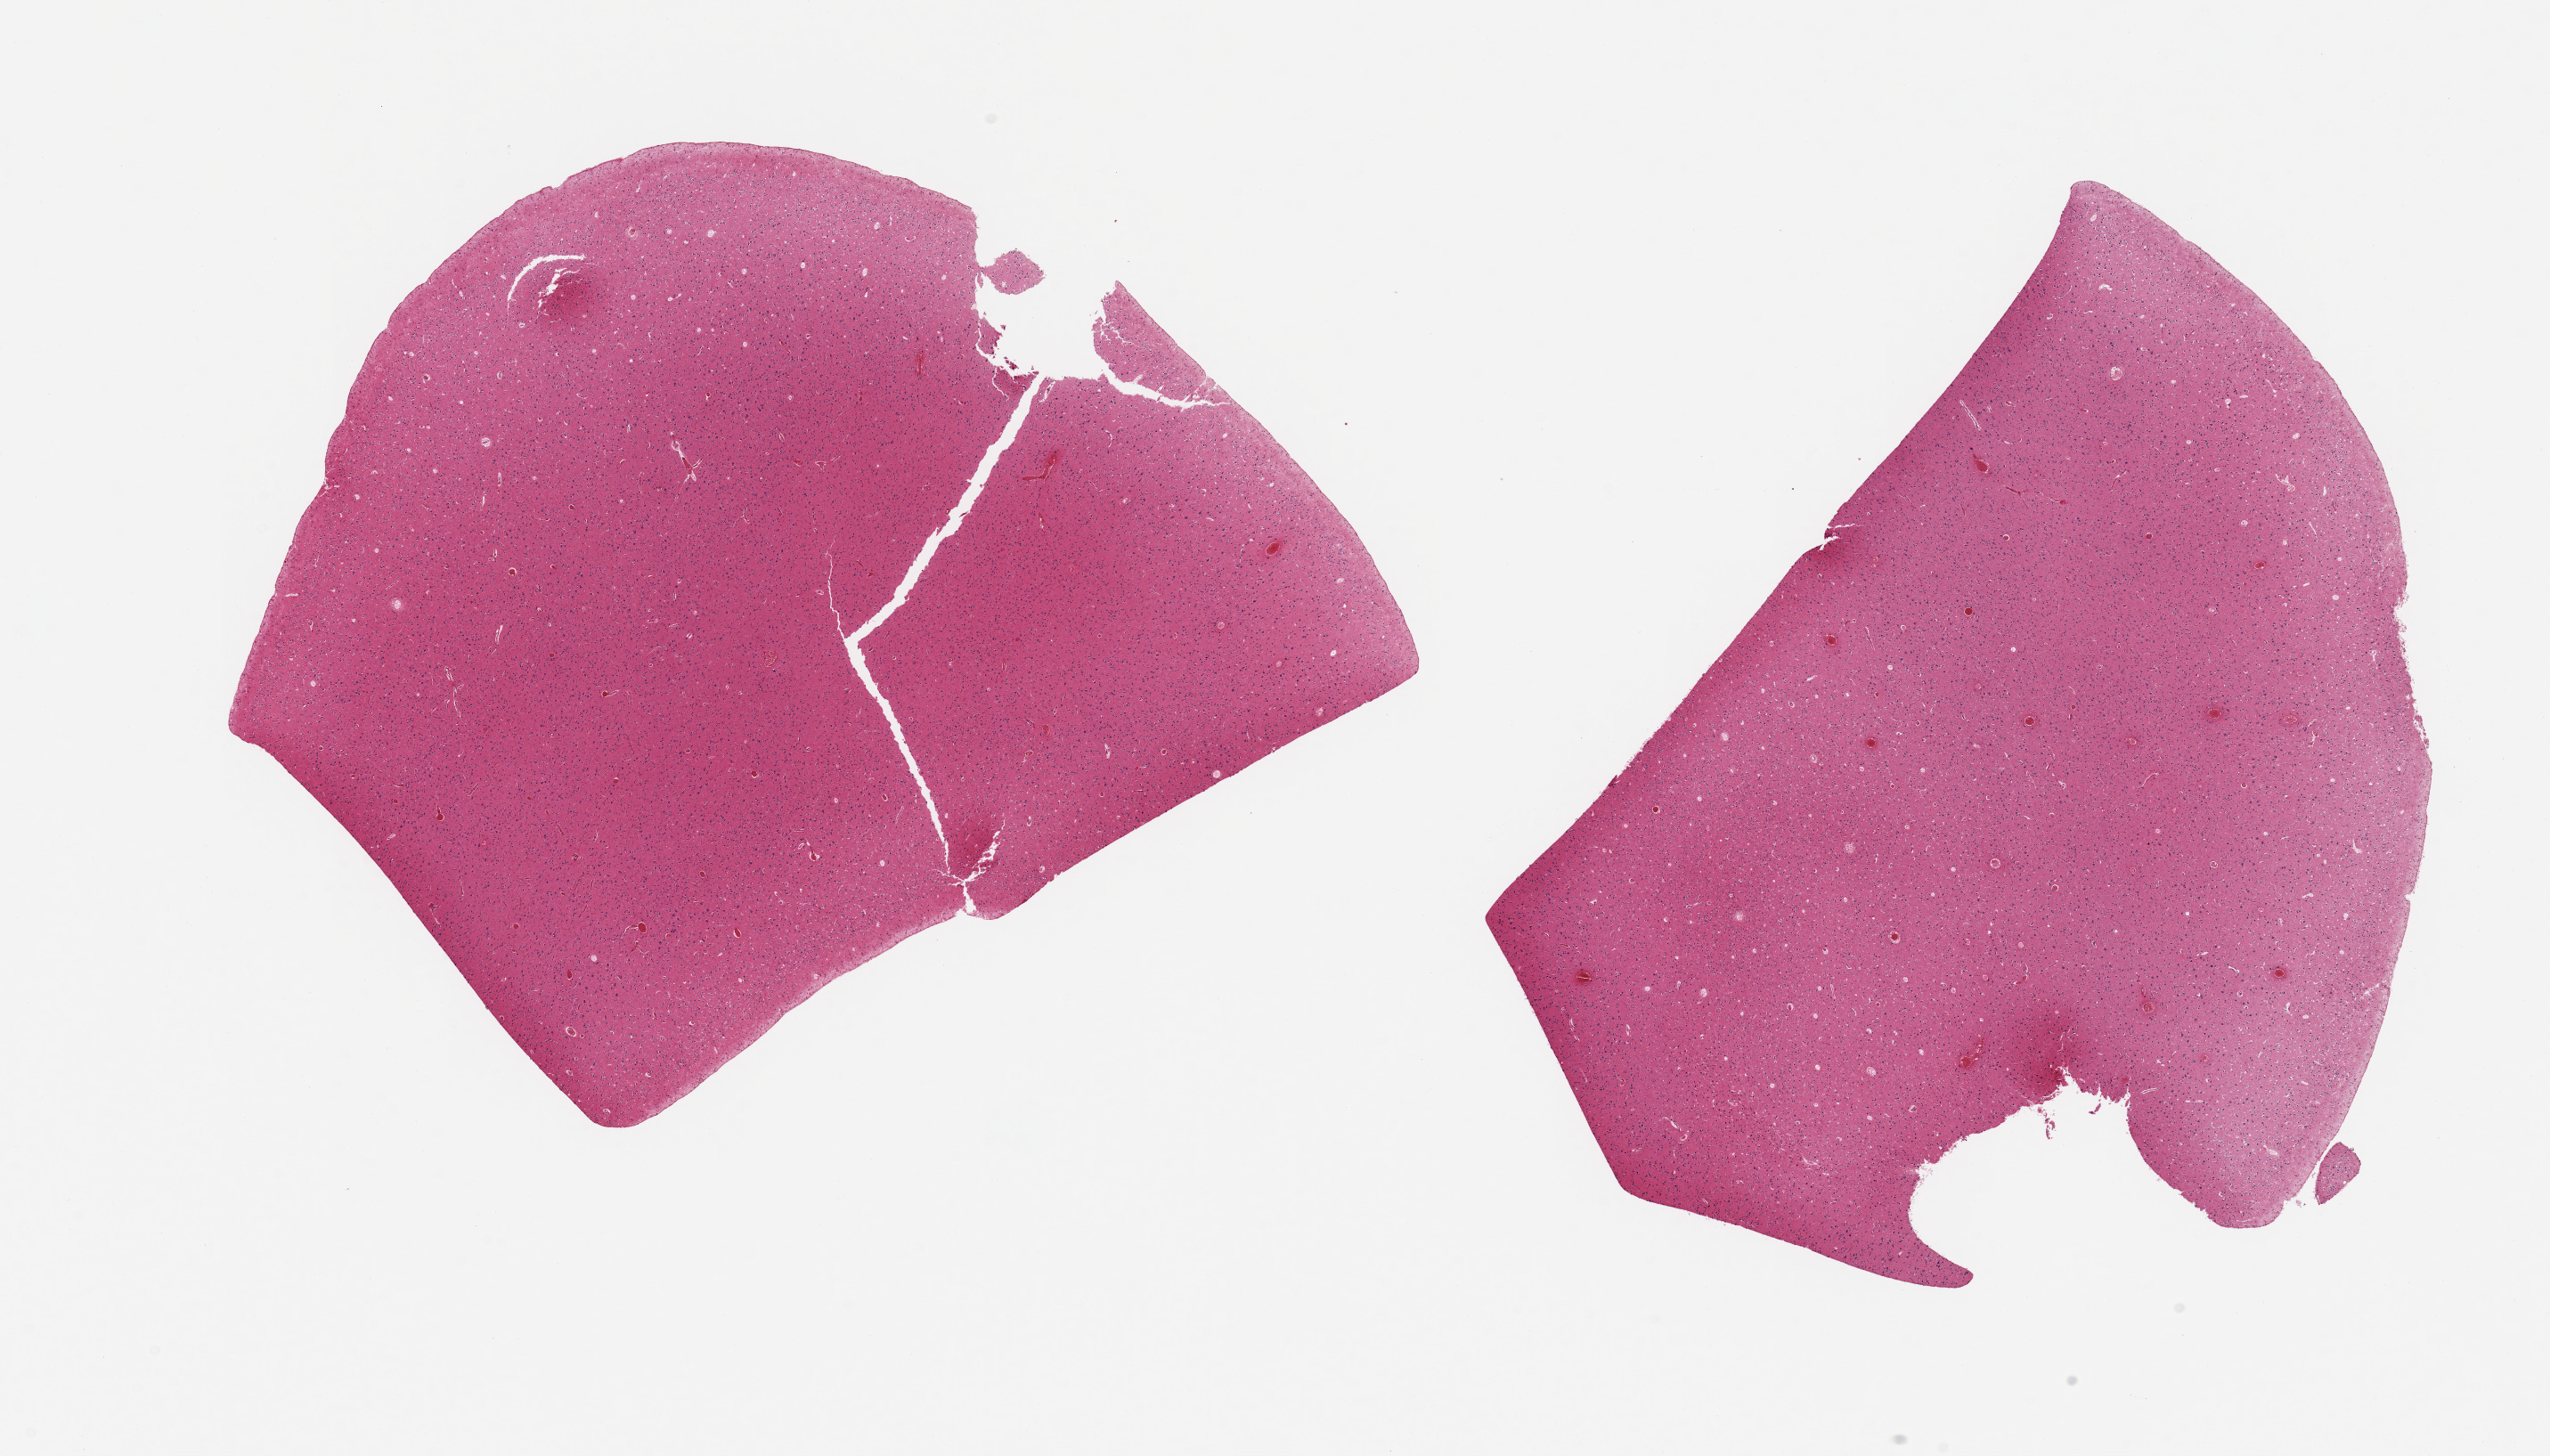
Digitized hematoxylin and eosin (H&E)-stained section, low-resolution overview of the scanned area, about 22.6 x 12.9 mm (acquisition: 20x scan); PAXgene-fixed paraffin-embedded (PFPE) section; sampled site (target tissue): cerebral cortex; tissue donor sample. Donor: male.
* reviewer comment on this tissue sample: 2 pieces, no abnormalities